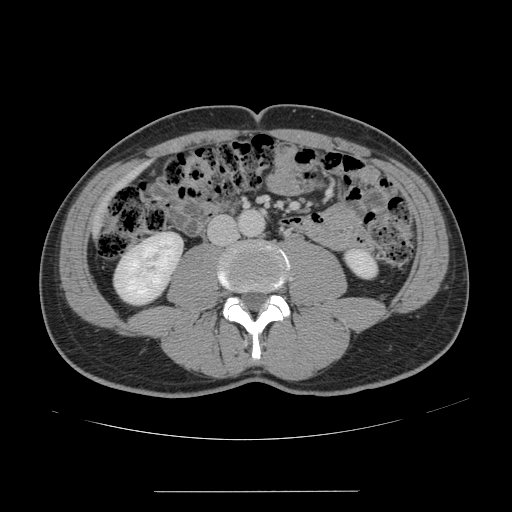
Contrast-enhanced abdominal CT, one axial slice. Position 26 of 178 along the scan axis. Intravenous contrast given. Soft-tissue window (W 400 / L 40 HU). 512 × 512 image matrix. Male patient, age 53 years. Case-level facts recorded for this patient, not image findings: diagnosis: colorectal cancer liver metastases, imaged before liver resection; multiple liver metastases: yes; largest metastasis: 2.4 cm; disease in both lobes: no.
Outlined on this slice (outlined manually by an expert reader):
- liver: box from (x=126, y=171) to (x=138, y=182) px